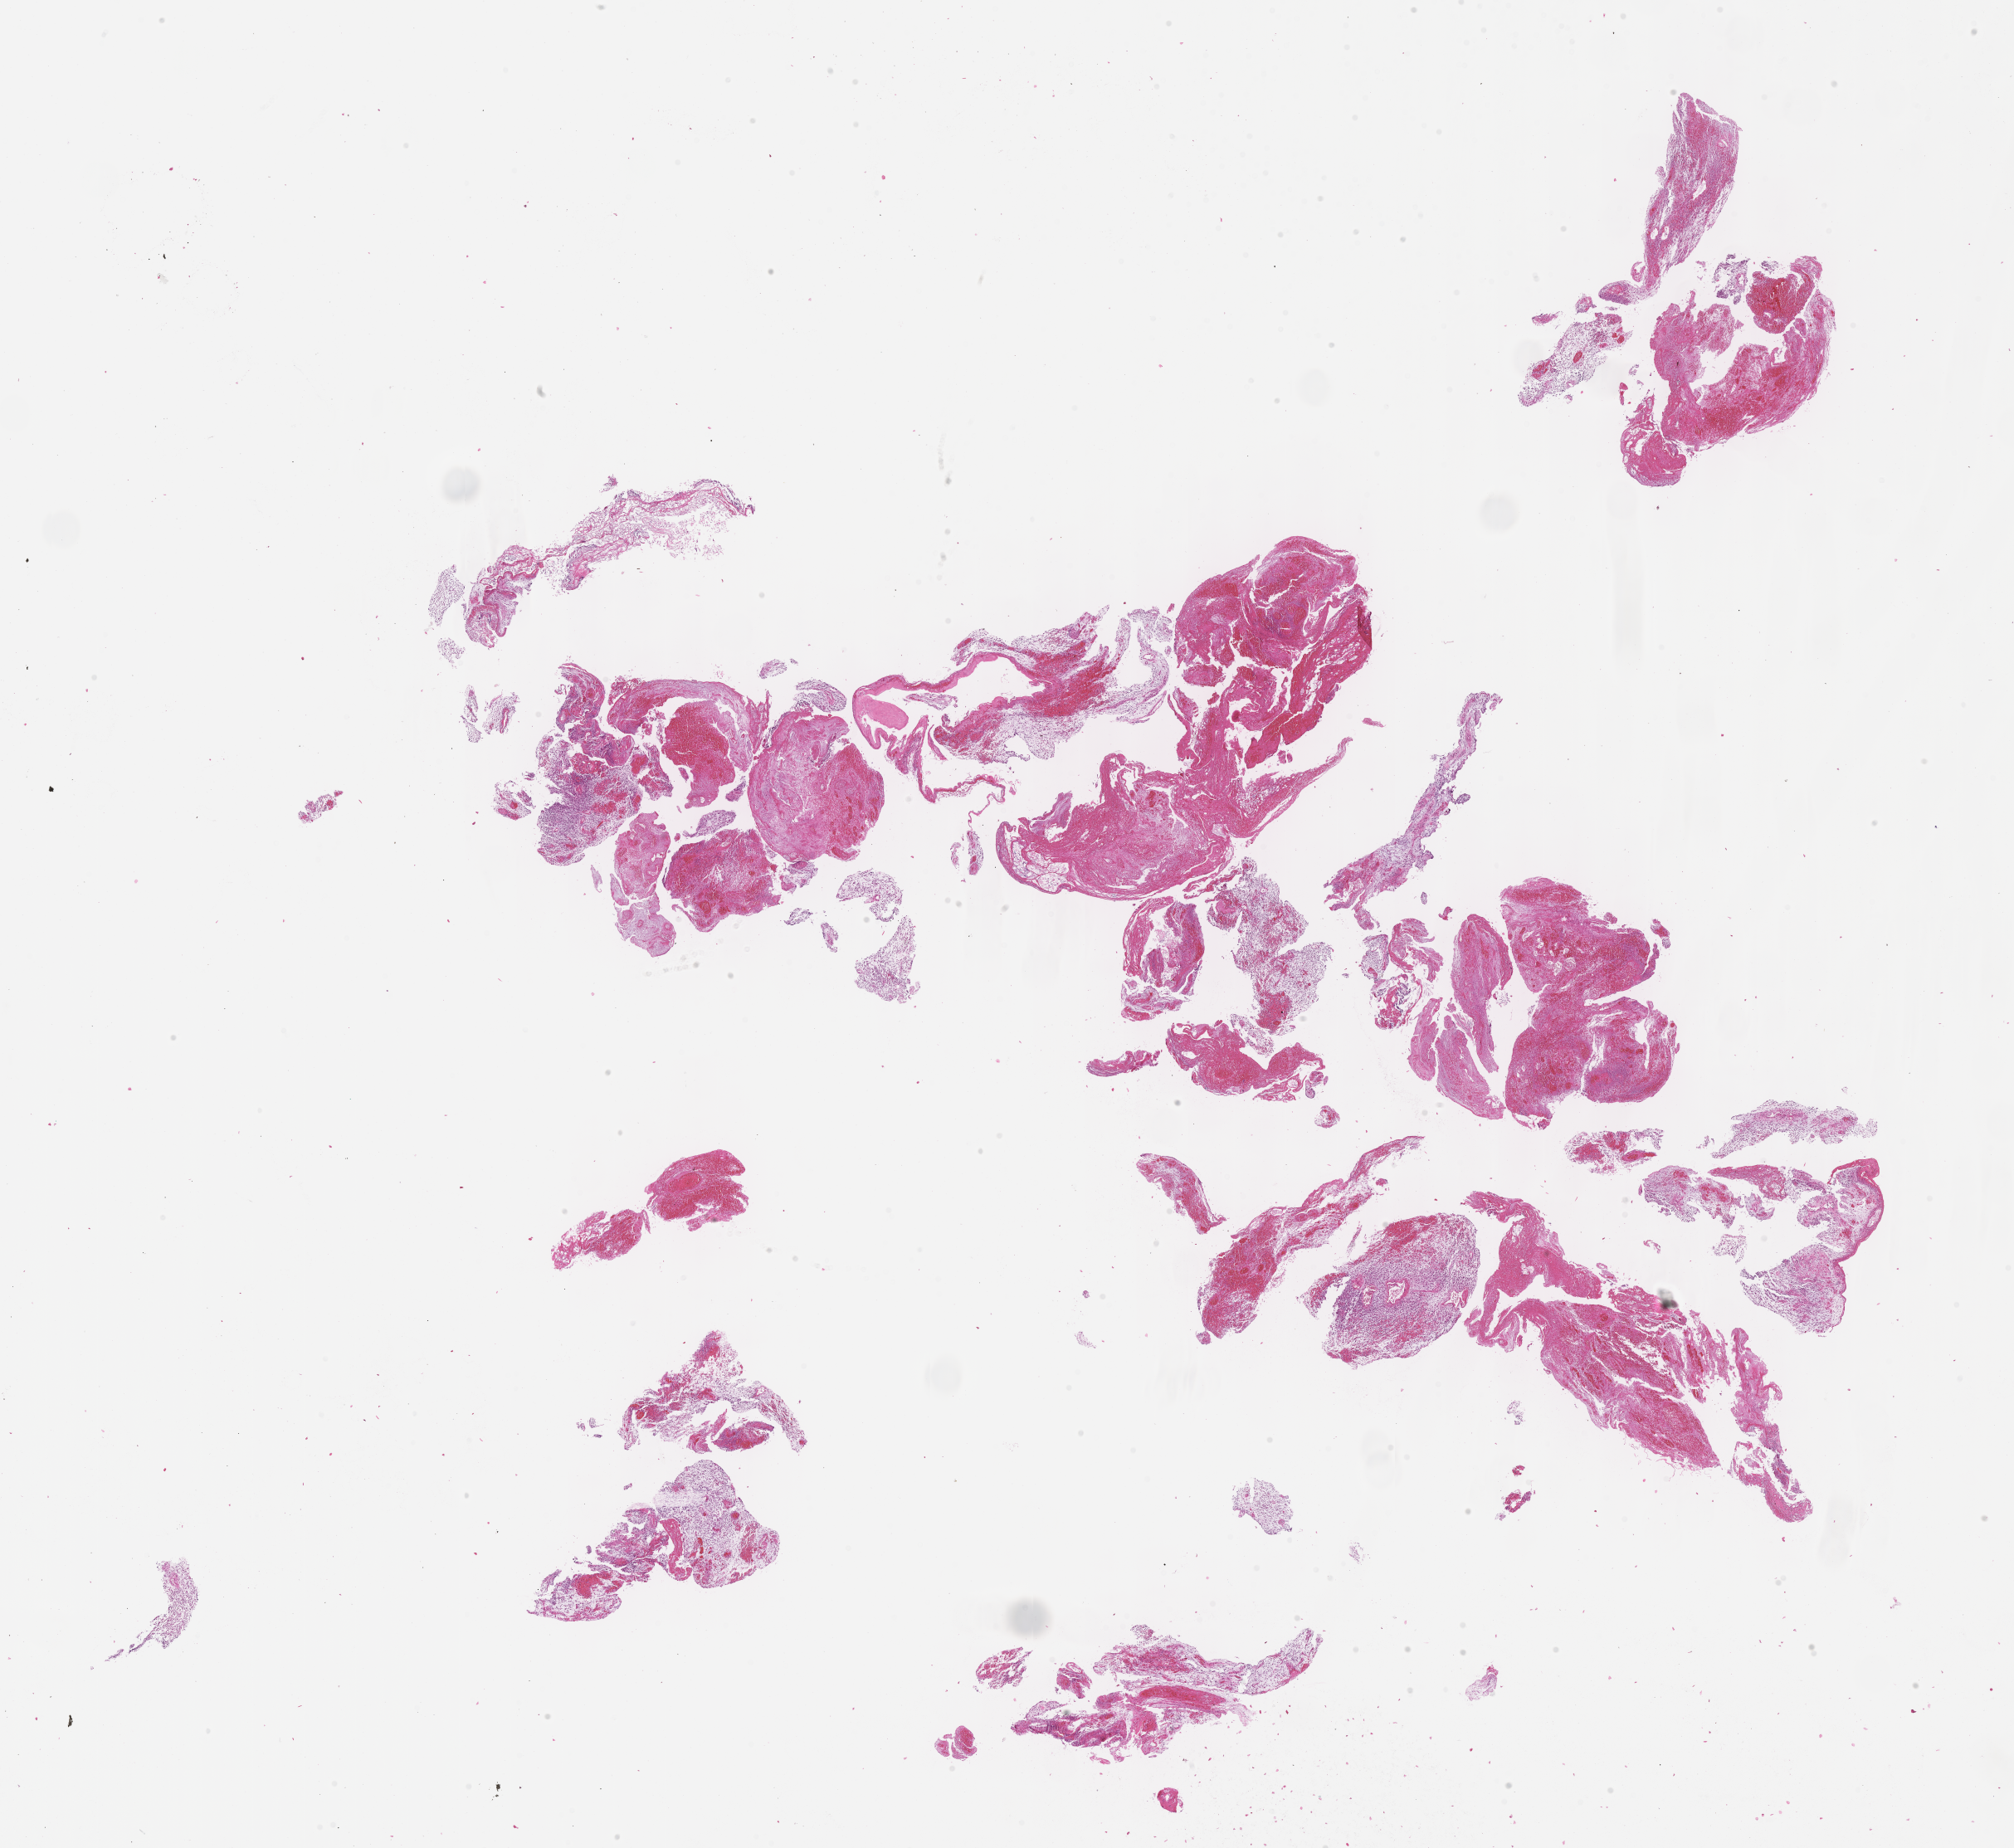
Digitized H&E-stained section of tumor tissue — shown as a low-resolution overview of the whole scanned area (about 19.6 x 18.0 mm), formalin-fixed paraffin-embedded section, site: soft tissue, ear-right (middle ear). Male patient, age at diagnosis 4.0 years.
Diagnosis: rhabdomyosarcoma; histological classification: embryonal rhabdomyosarcoma.